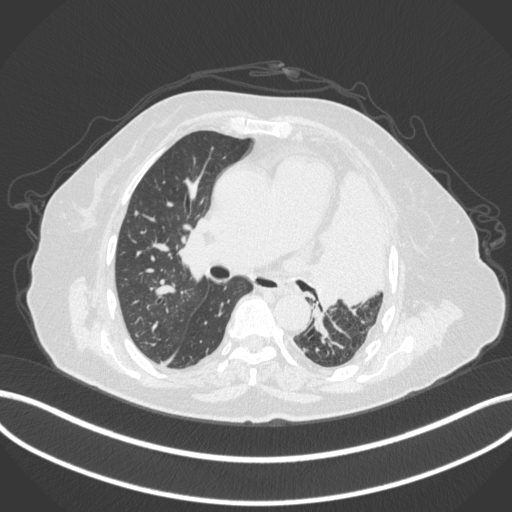
Chest CT, one axial slice; position 218 of 399 along the scan axis; reconstruction kernel B31f; 120 kVp; lung window (W 1500 / L -600 HU); 512 × 512 image matrix, field of view 400 × 400 mm. Female patient, age 75 years. From the clinical record (not read from this slice): clinical TNM (as recorded): T3 N3 M1.
Outlined on this slice (rectangle marked by the reading radiologist):
- lung tumour (recorded histology: adenocarcinoma): bounding box [x1, y1, x2, y2] px = [310, 158, 393, 307]